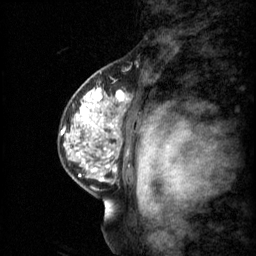
Breast MRI (dynamic contrast-enhanced), one sagittal slice. Slice 43 of 60 in the series (ordered by position). 3 images stored at this slice position (order not interpretable as contrast timing). 1.5 T. TE 4.2 ms, TR 11 ms. 2 mm slice thickness. 256 × 256 image matrix, field of view 200 × 200 mm. Female patient, age 48 years.
Structures marked on this image (semi-automatic segmentation, software-assisted and operator-edited):
- analysis volume of interest (the breast-tissue region the enhancement analysis was run in; not a lesion): bounding box <69,74,141,147> (left, top, right, bottom; pixels)
- tumour enhancement mask (voxels above the 70 % enhancement threshold inside the analysis volume of interest): <81,88,129,137>